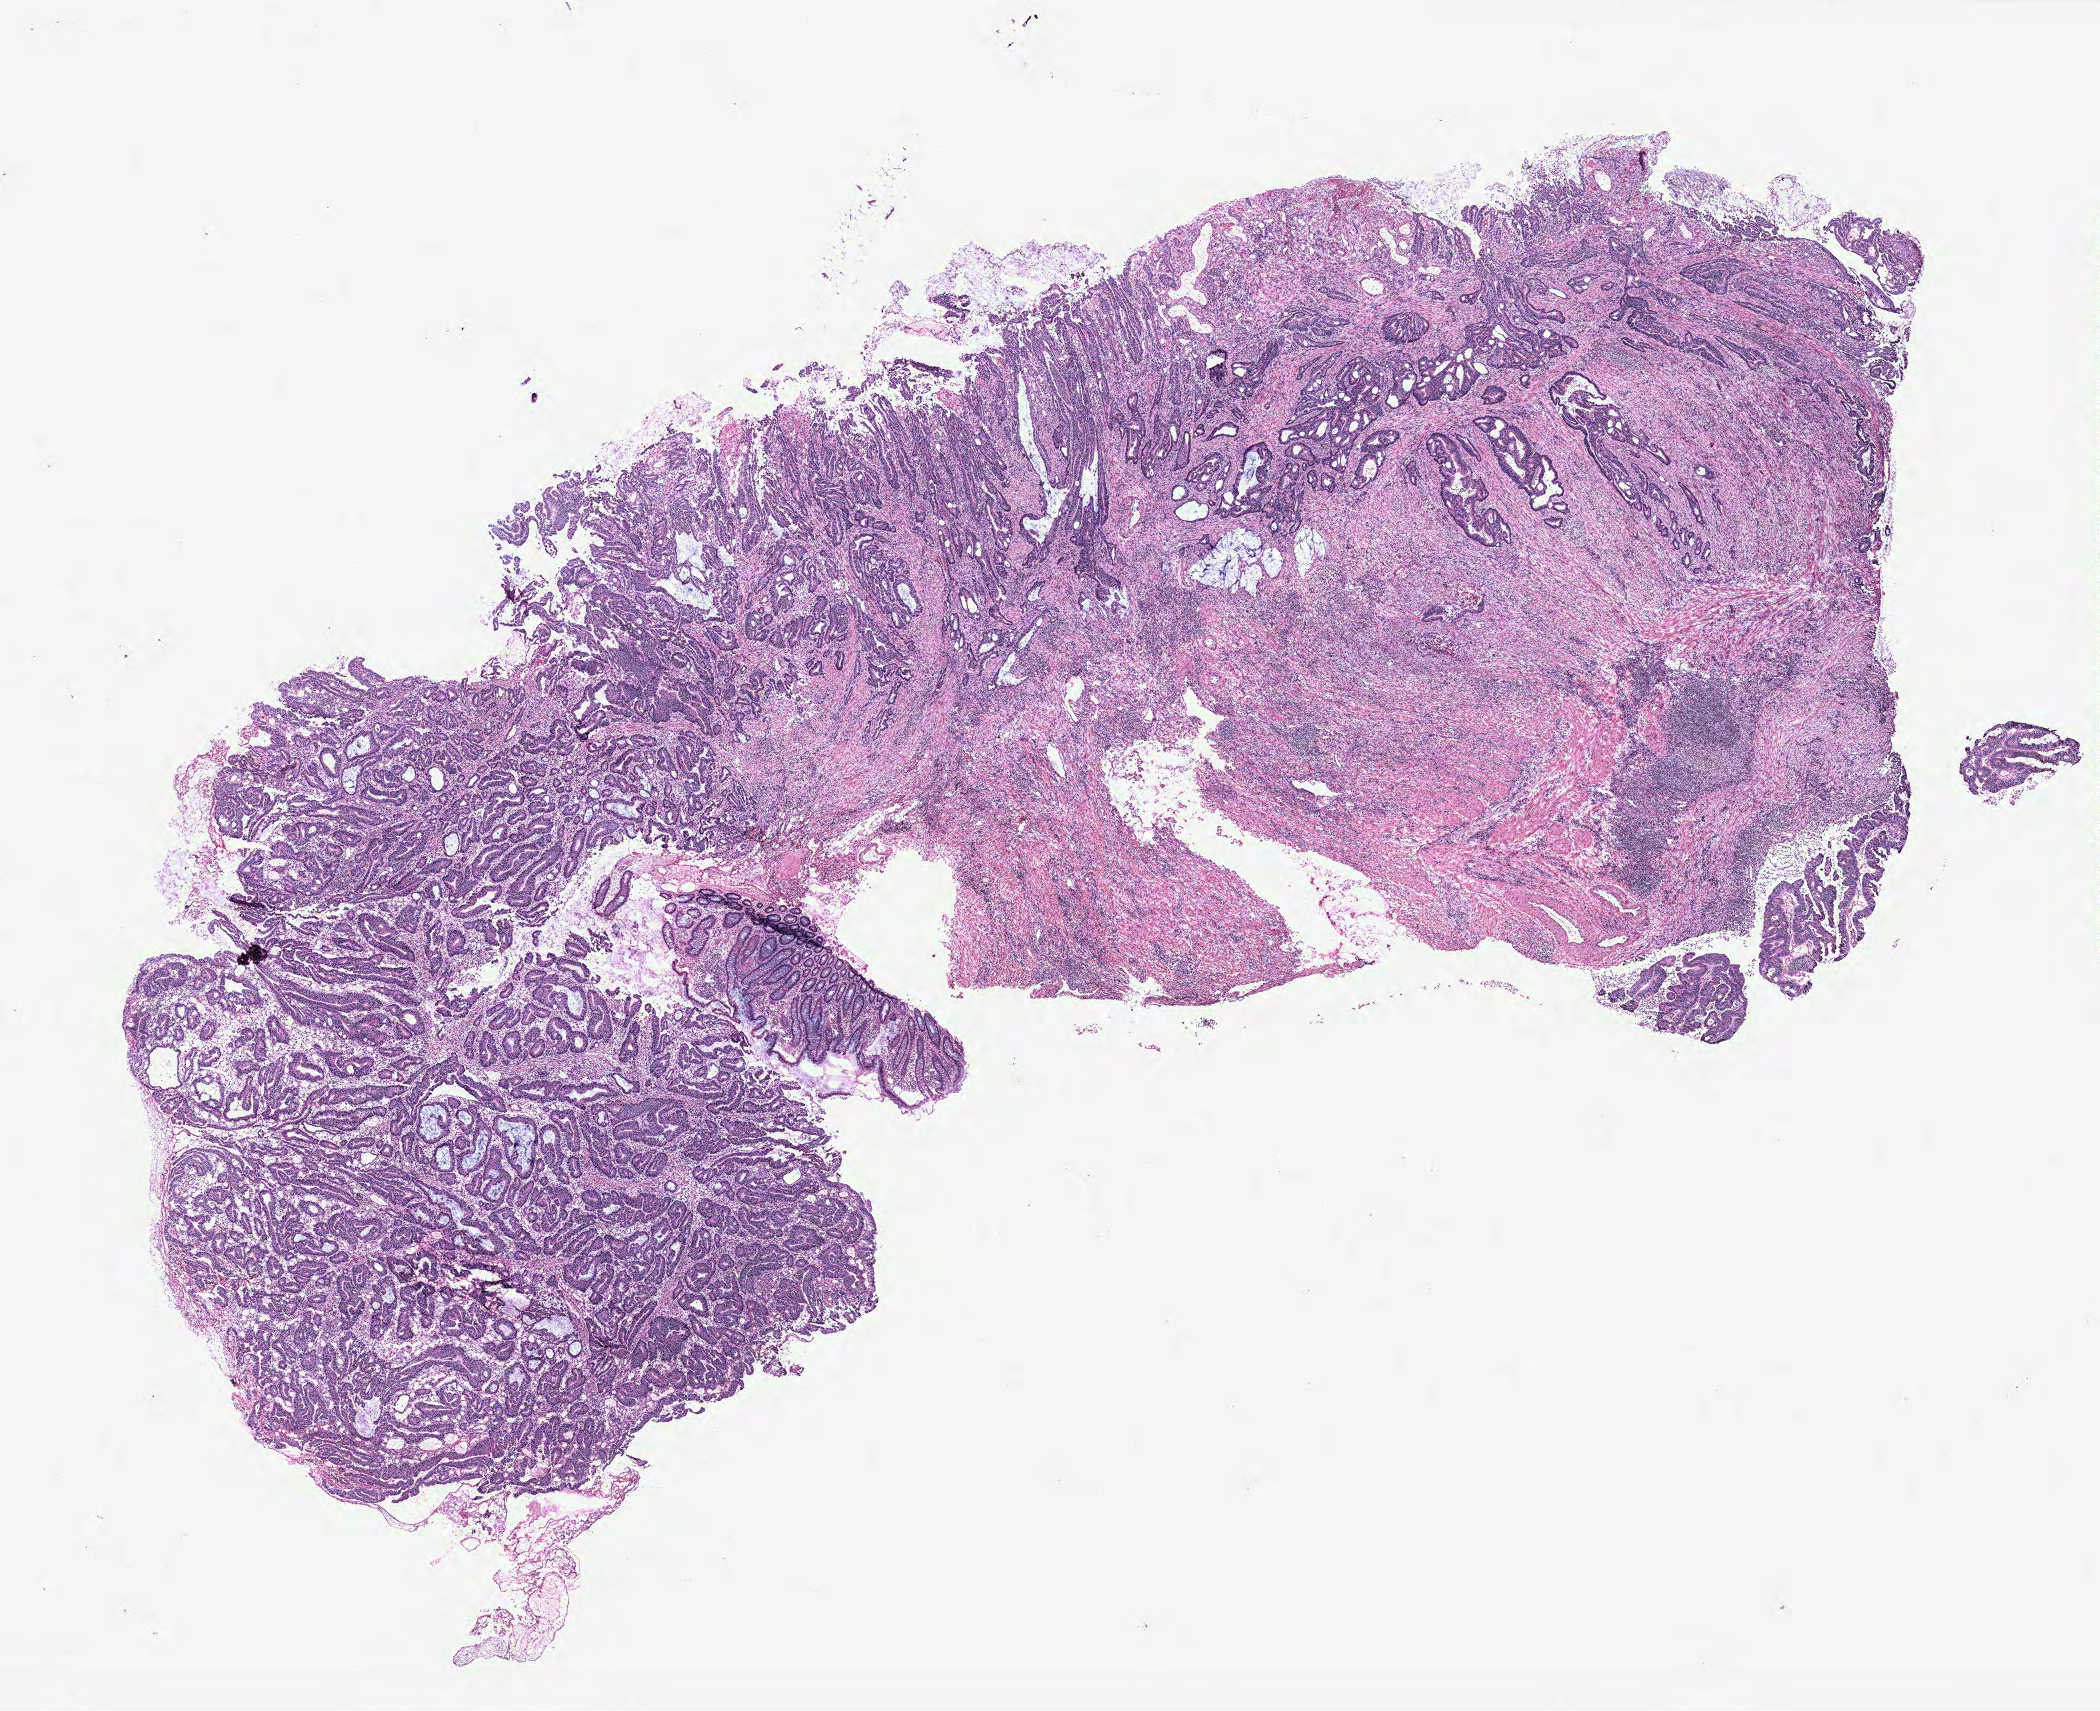
H&E-stained whole-slide image, a low-resolution overview of the entire scanned area, about 16.8 x 13.7 mm; colon, normal (non-tumour) tissue. 87-year-old male patient.
This section: normal (non-tumour) tissue from the same patient. Patient diagnosis: Adenocarcinoma, NOS.